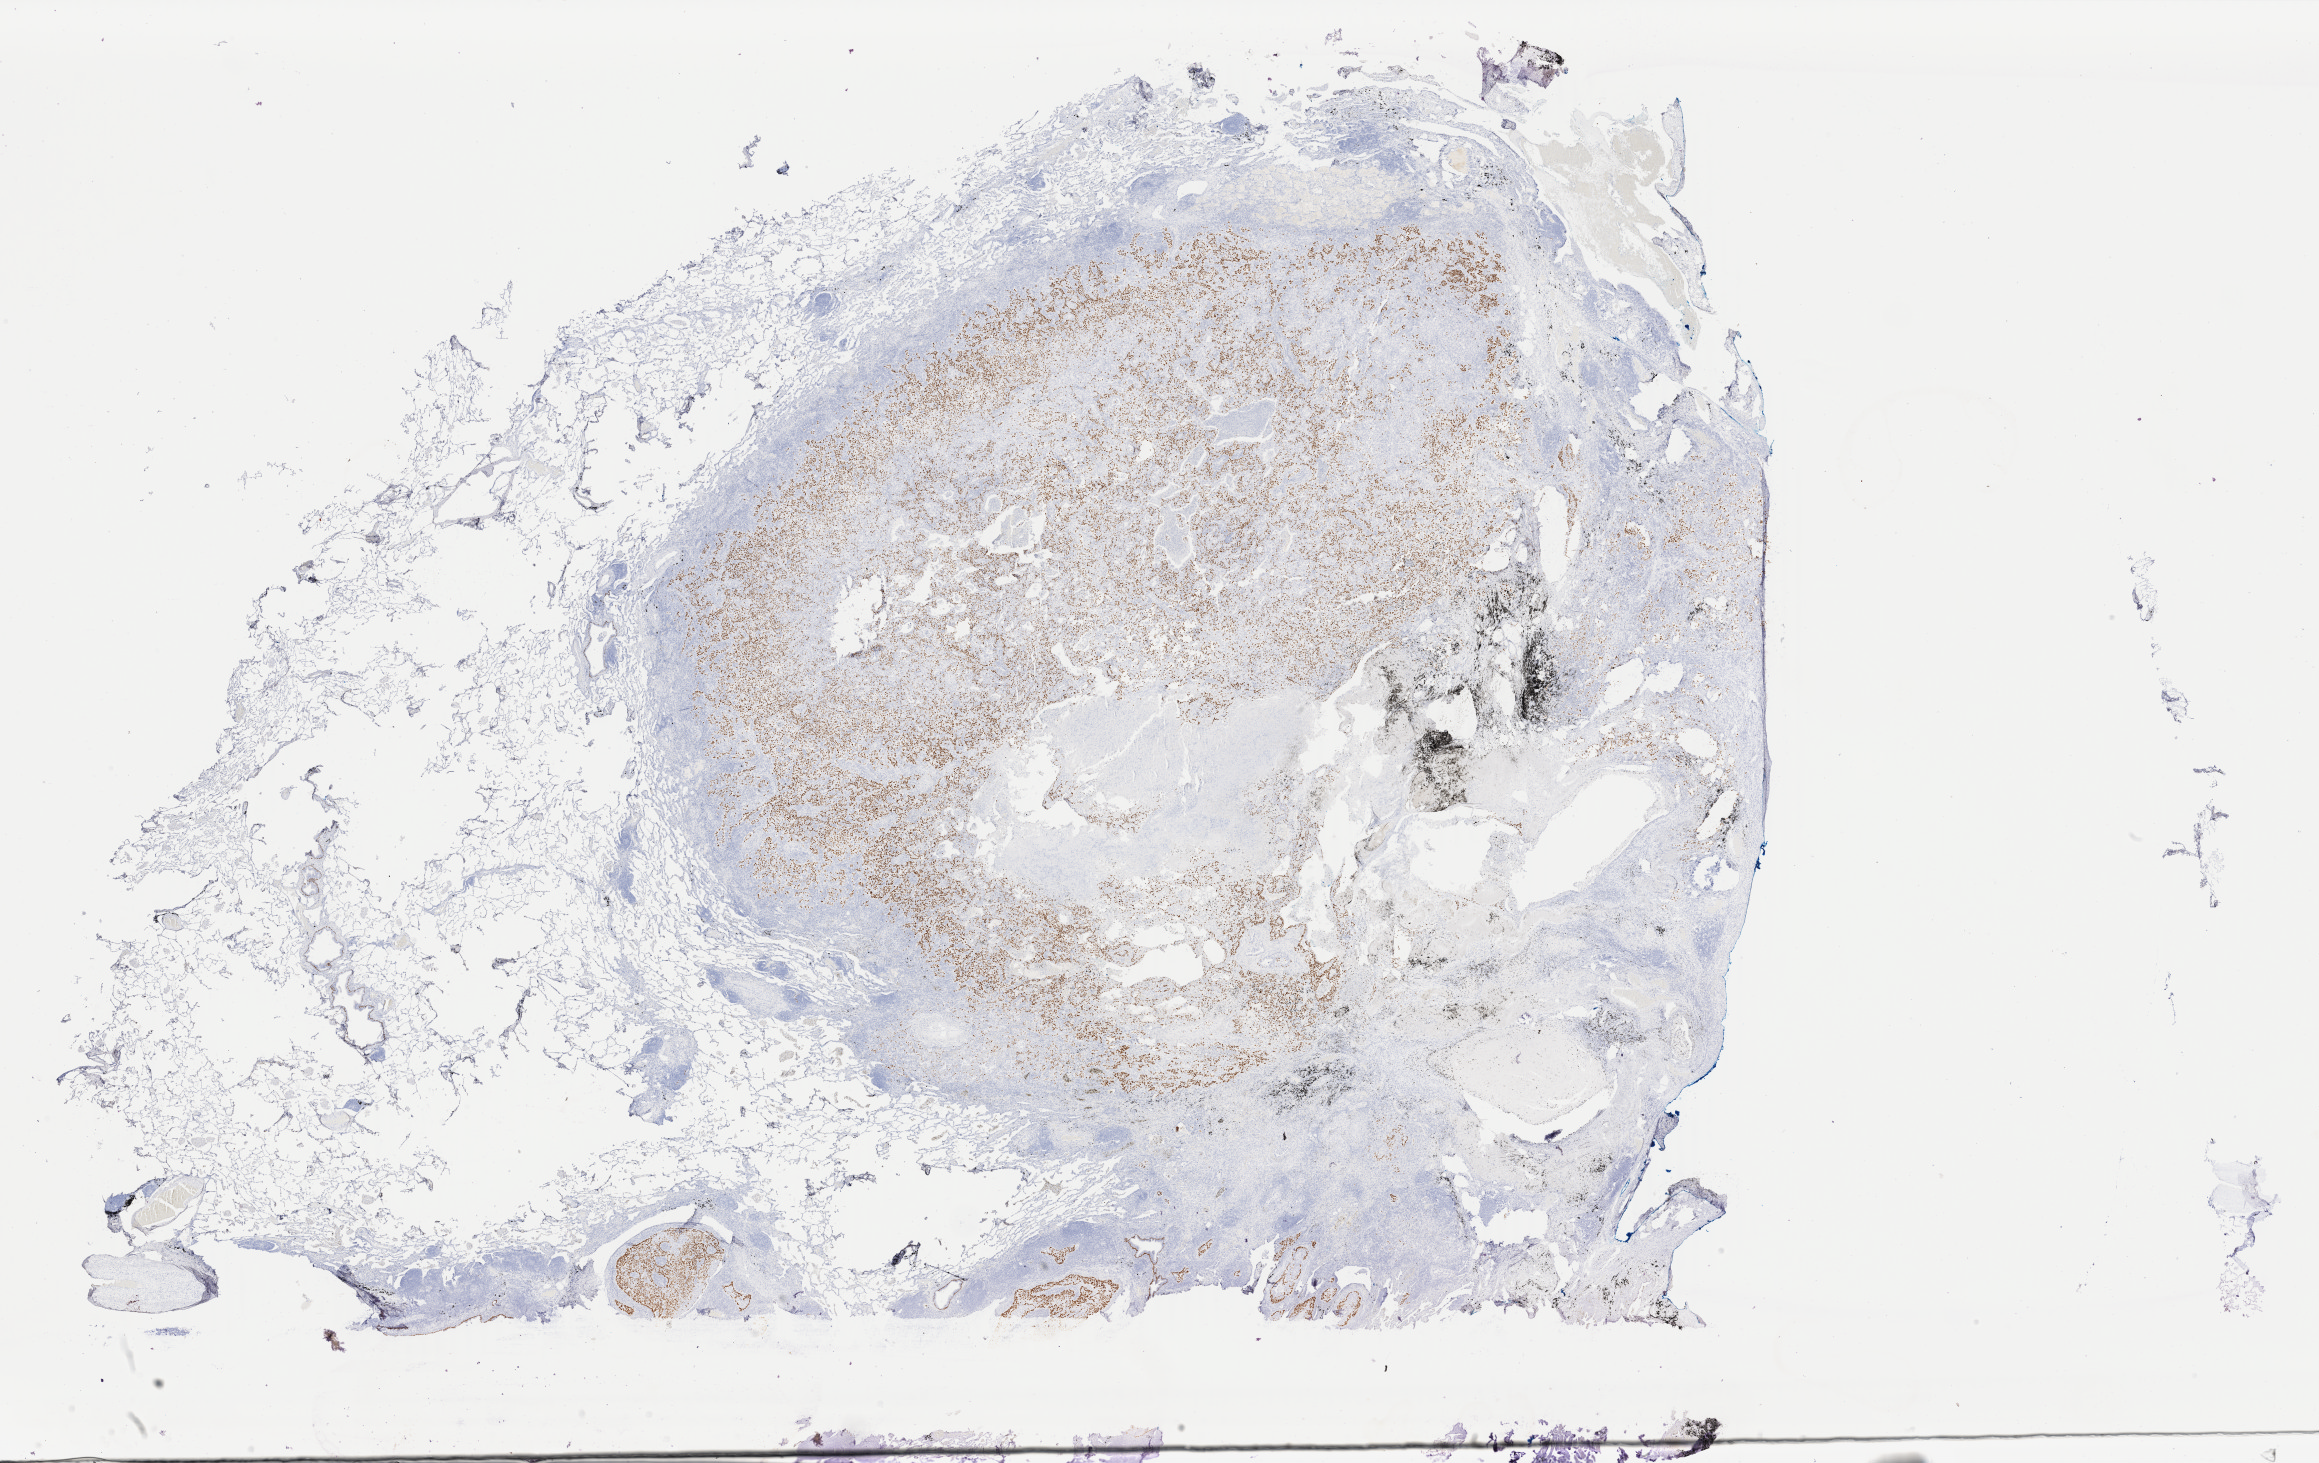
Immunohistochemistry (IHC) whole-slide image stained for p40 — a low-resolution overview of the entire scanned area, about 36.9 x 23.3 mm, tumor tissue, anatomic site: lung (right). Patient: male, age 59 years.
- diagnosis: Adenosquamous carcinoma